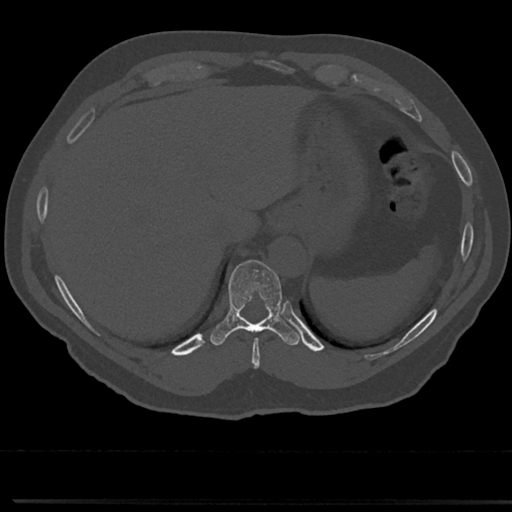
CT including the spine, one axial slice. Position 263 of 817 along the scan axis. 120 kVp. Bone window (W 1800 / L 400 HU). 0.5 mm slice thickness. 512 × 512 image matrix. Patient: male, 61 years. From the clinical record (not read from this slice): primary cancer: prostate.
Structures marked on this image (semi-automatically segmented with operator editing):
- T10 vertebra: bounding box <216,261,283,340> (left, top, right, bottom; pixels)
- T9 vertebra: <247,330,267,355>